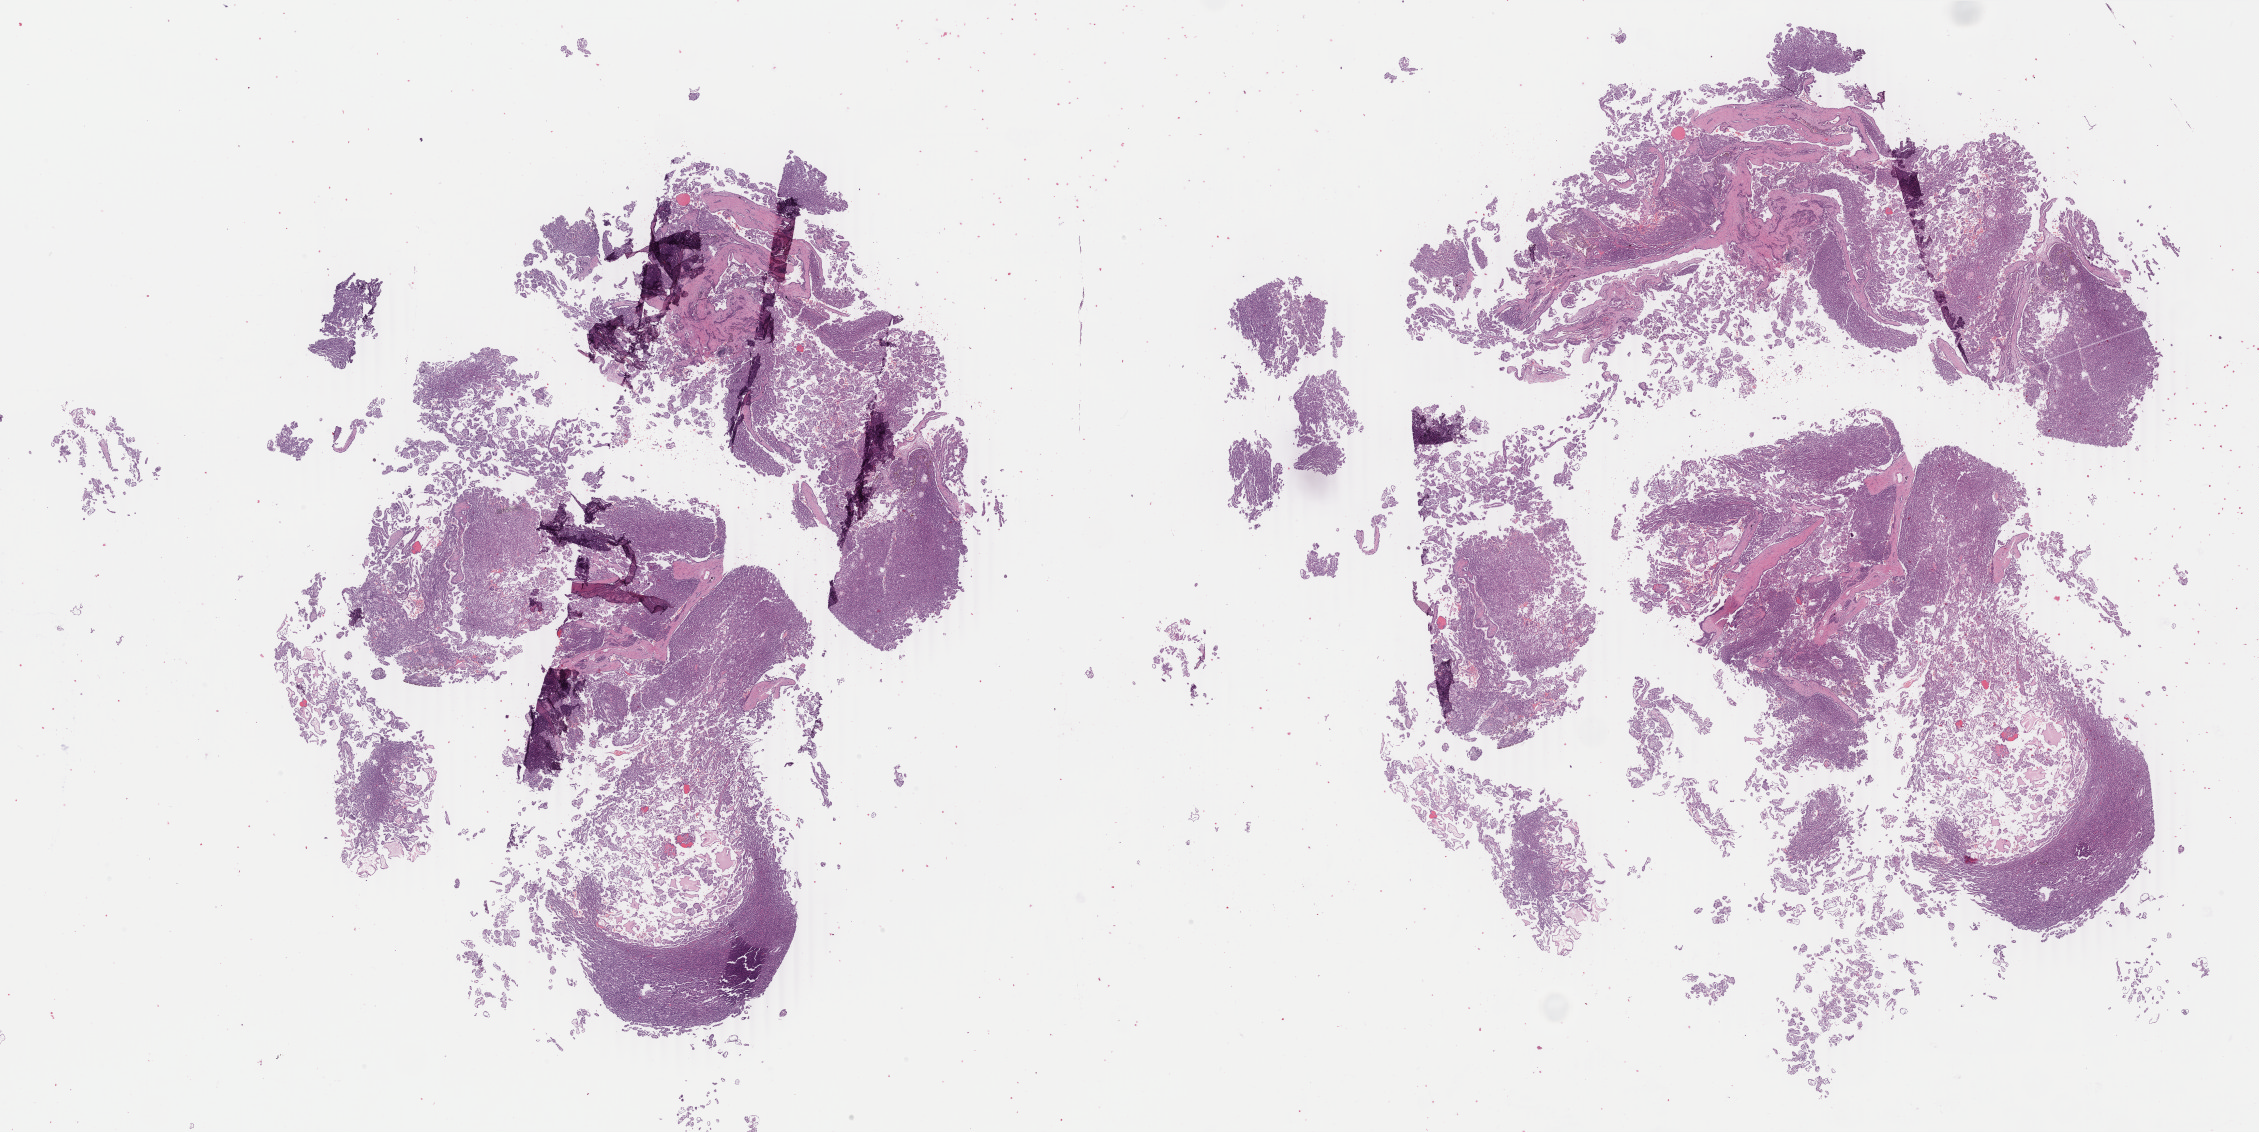
Digitized Hematoxylin and eosin (H&E) stained tissue section (whole slide), shown as a low-resolution overview of the whole scanned area (about 35.9 x 18.0 mm, acquisition: 40x scan), formalin-fixed paraffin-embedded (FFPE) diagnostic section, primary tumour sample from the kidney. Male, age 79 years at initial diagnosis.
* histologic diagnosis: Papillary adenocarcinoma, NOS
* AJCC pathologic stage: III (7th edition)